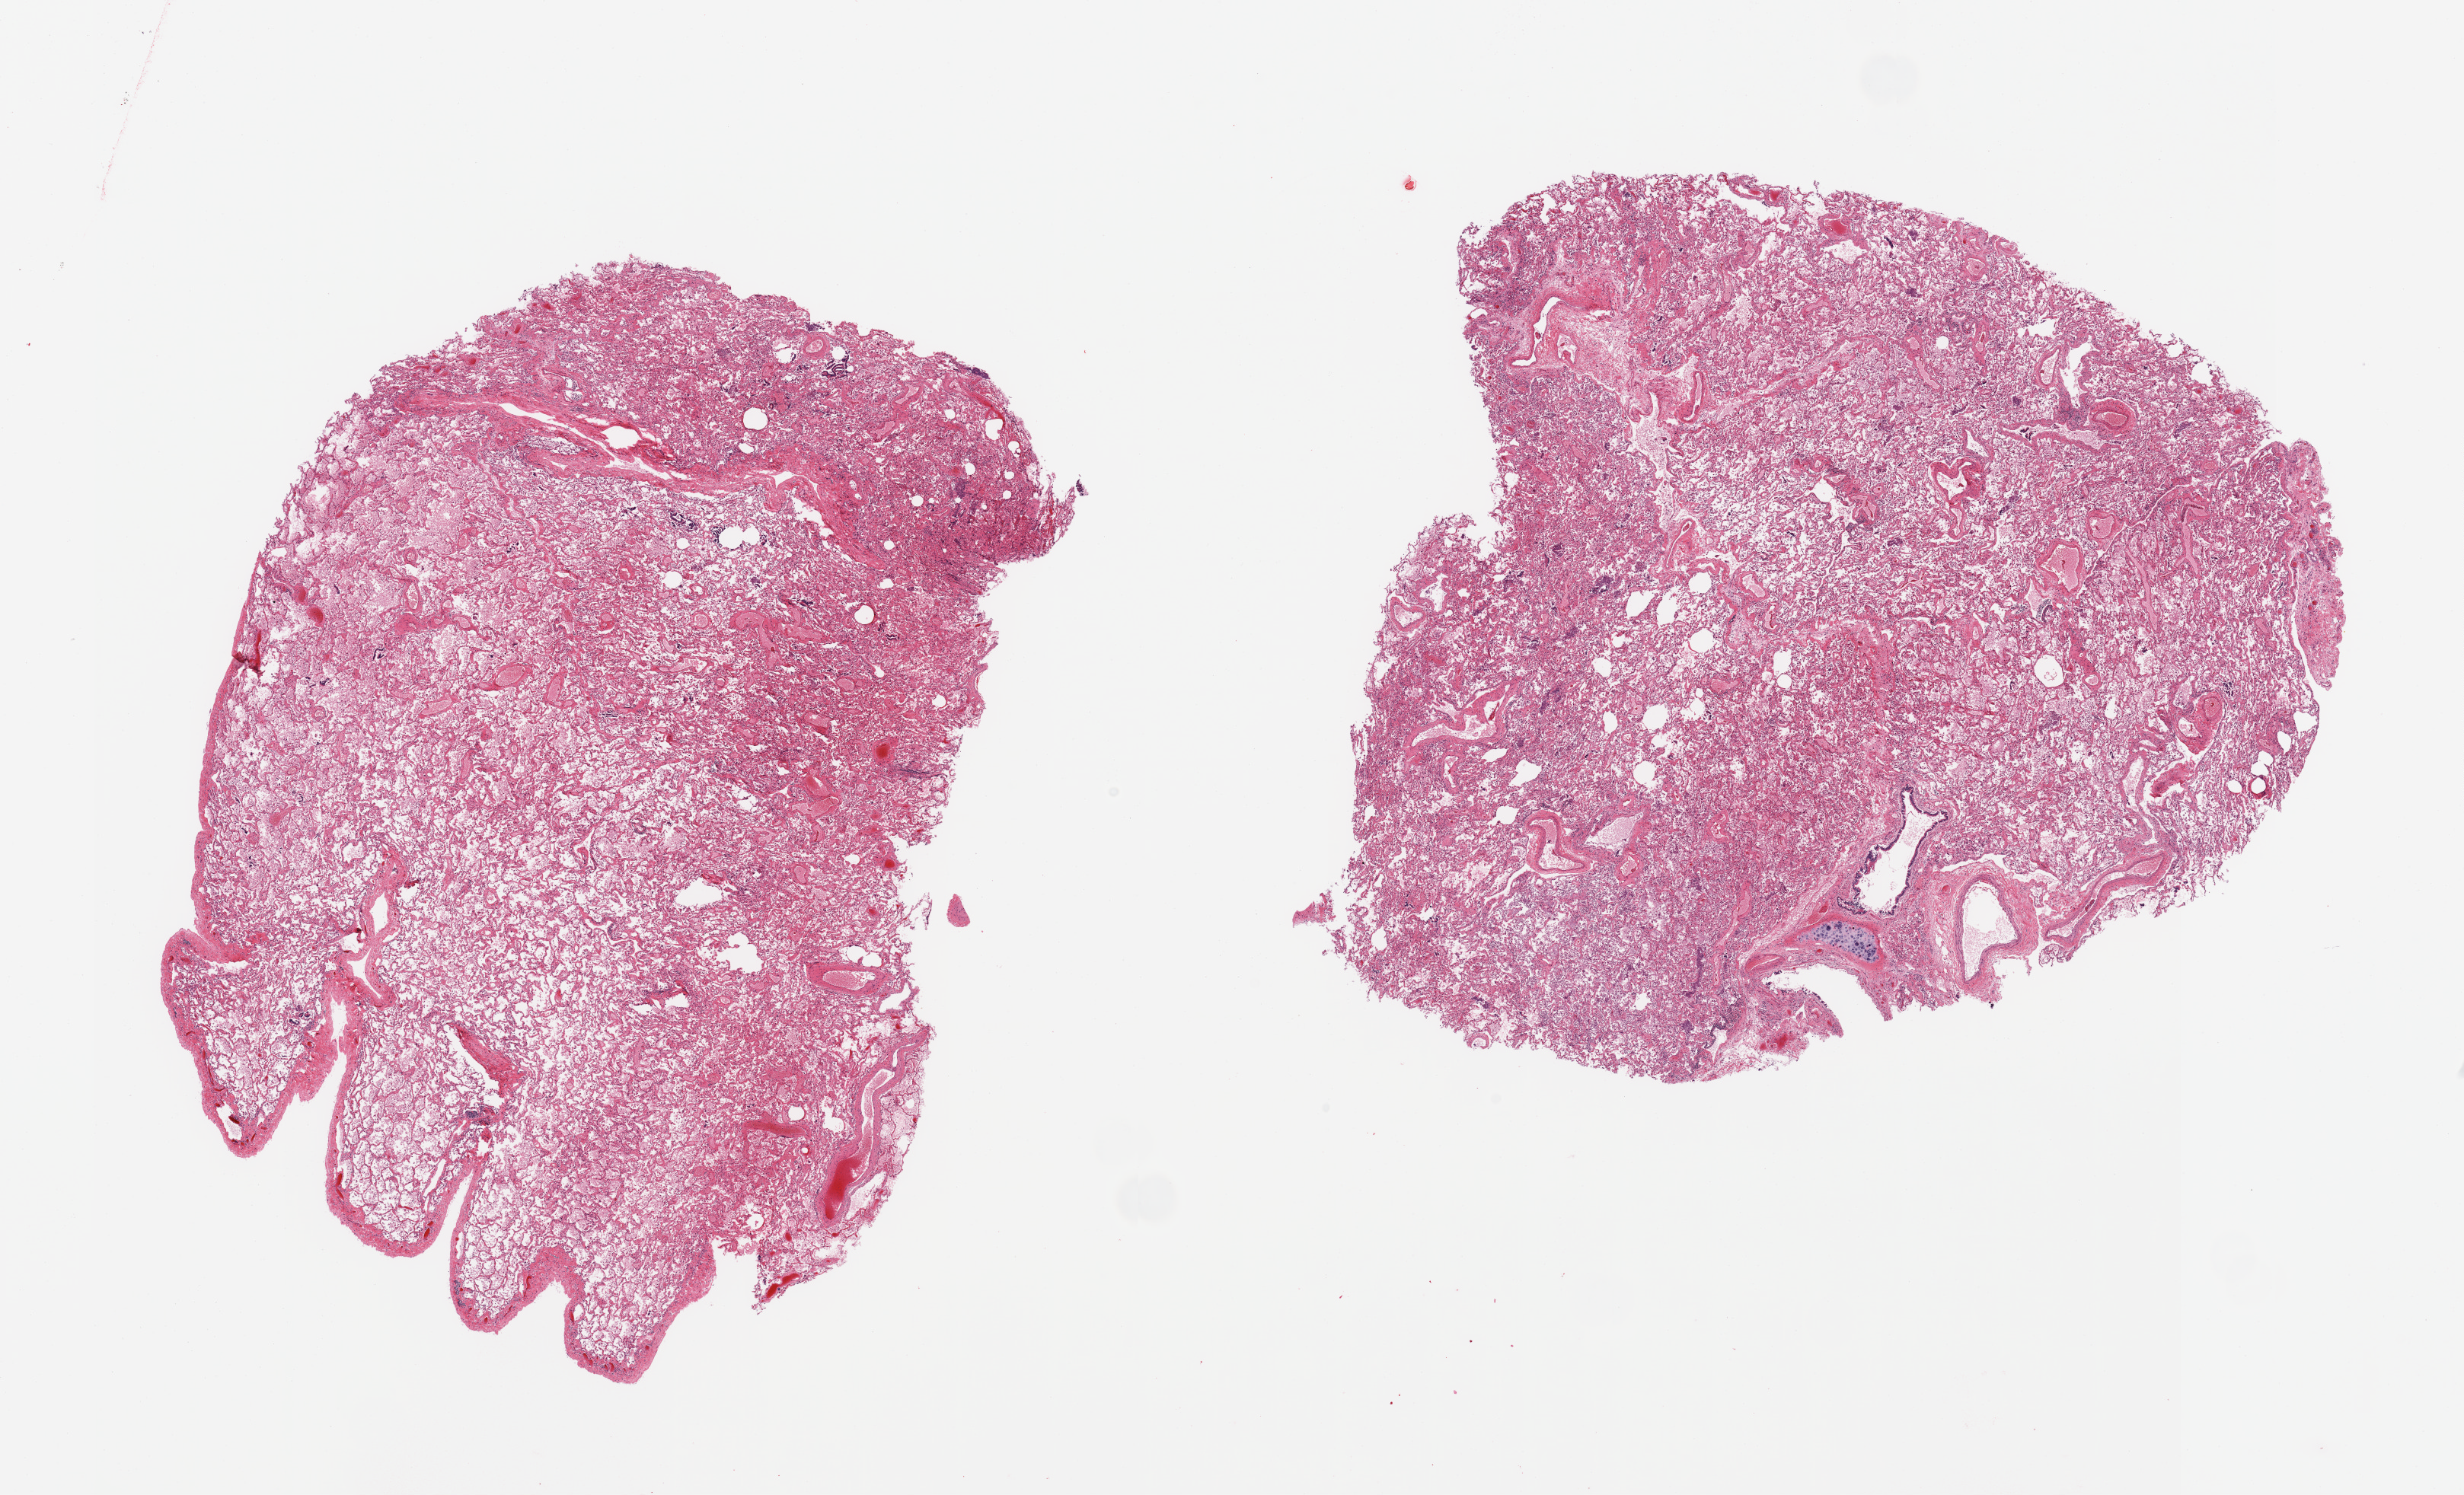
Whole-slide image, haematoxylin and eosin stain, low-resolution overview of the scanned area, about 25.6 x 15.5 mm, PAXgene-fixed paraffin-embedded (PFPE) section, section of lung (target tissue), donor tissue sample. Female donor.
Reviewer comment on this tissue sample: 2 pieces, moderate alveolar edema.